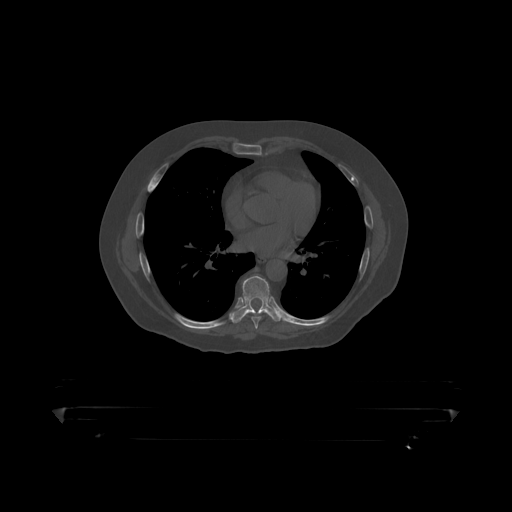
CT including the spine, one axial slice. Slice 265 of 390 in the series (ordered by position). Reconstruction kernel STANDARD. 120 kVp. Bone window (W 1800 / L 400 HU). 512 × 512 image matrix, field of view 650 × 650 mm. Male patient, age 60 years. From the clinical record (not read from this slice): primary cancer: prostate.
Outlined on this slice (semi-automatic segmentation, software-assisted and operator-edited):
- T6 vertebra: bounding box [x1, y1, x2, y2] px = [245, 300, 251, 306]
- T7 vertebra: [252, 312, 264, 319]
- T8 vertebra: [232, 276, 278, 318]